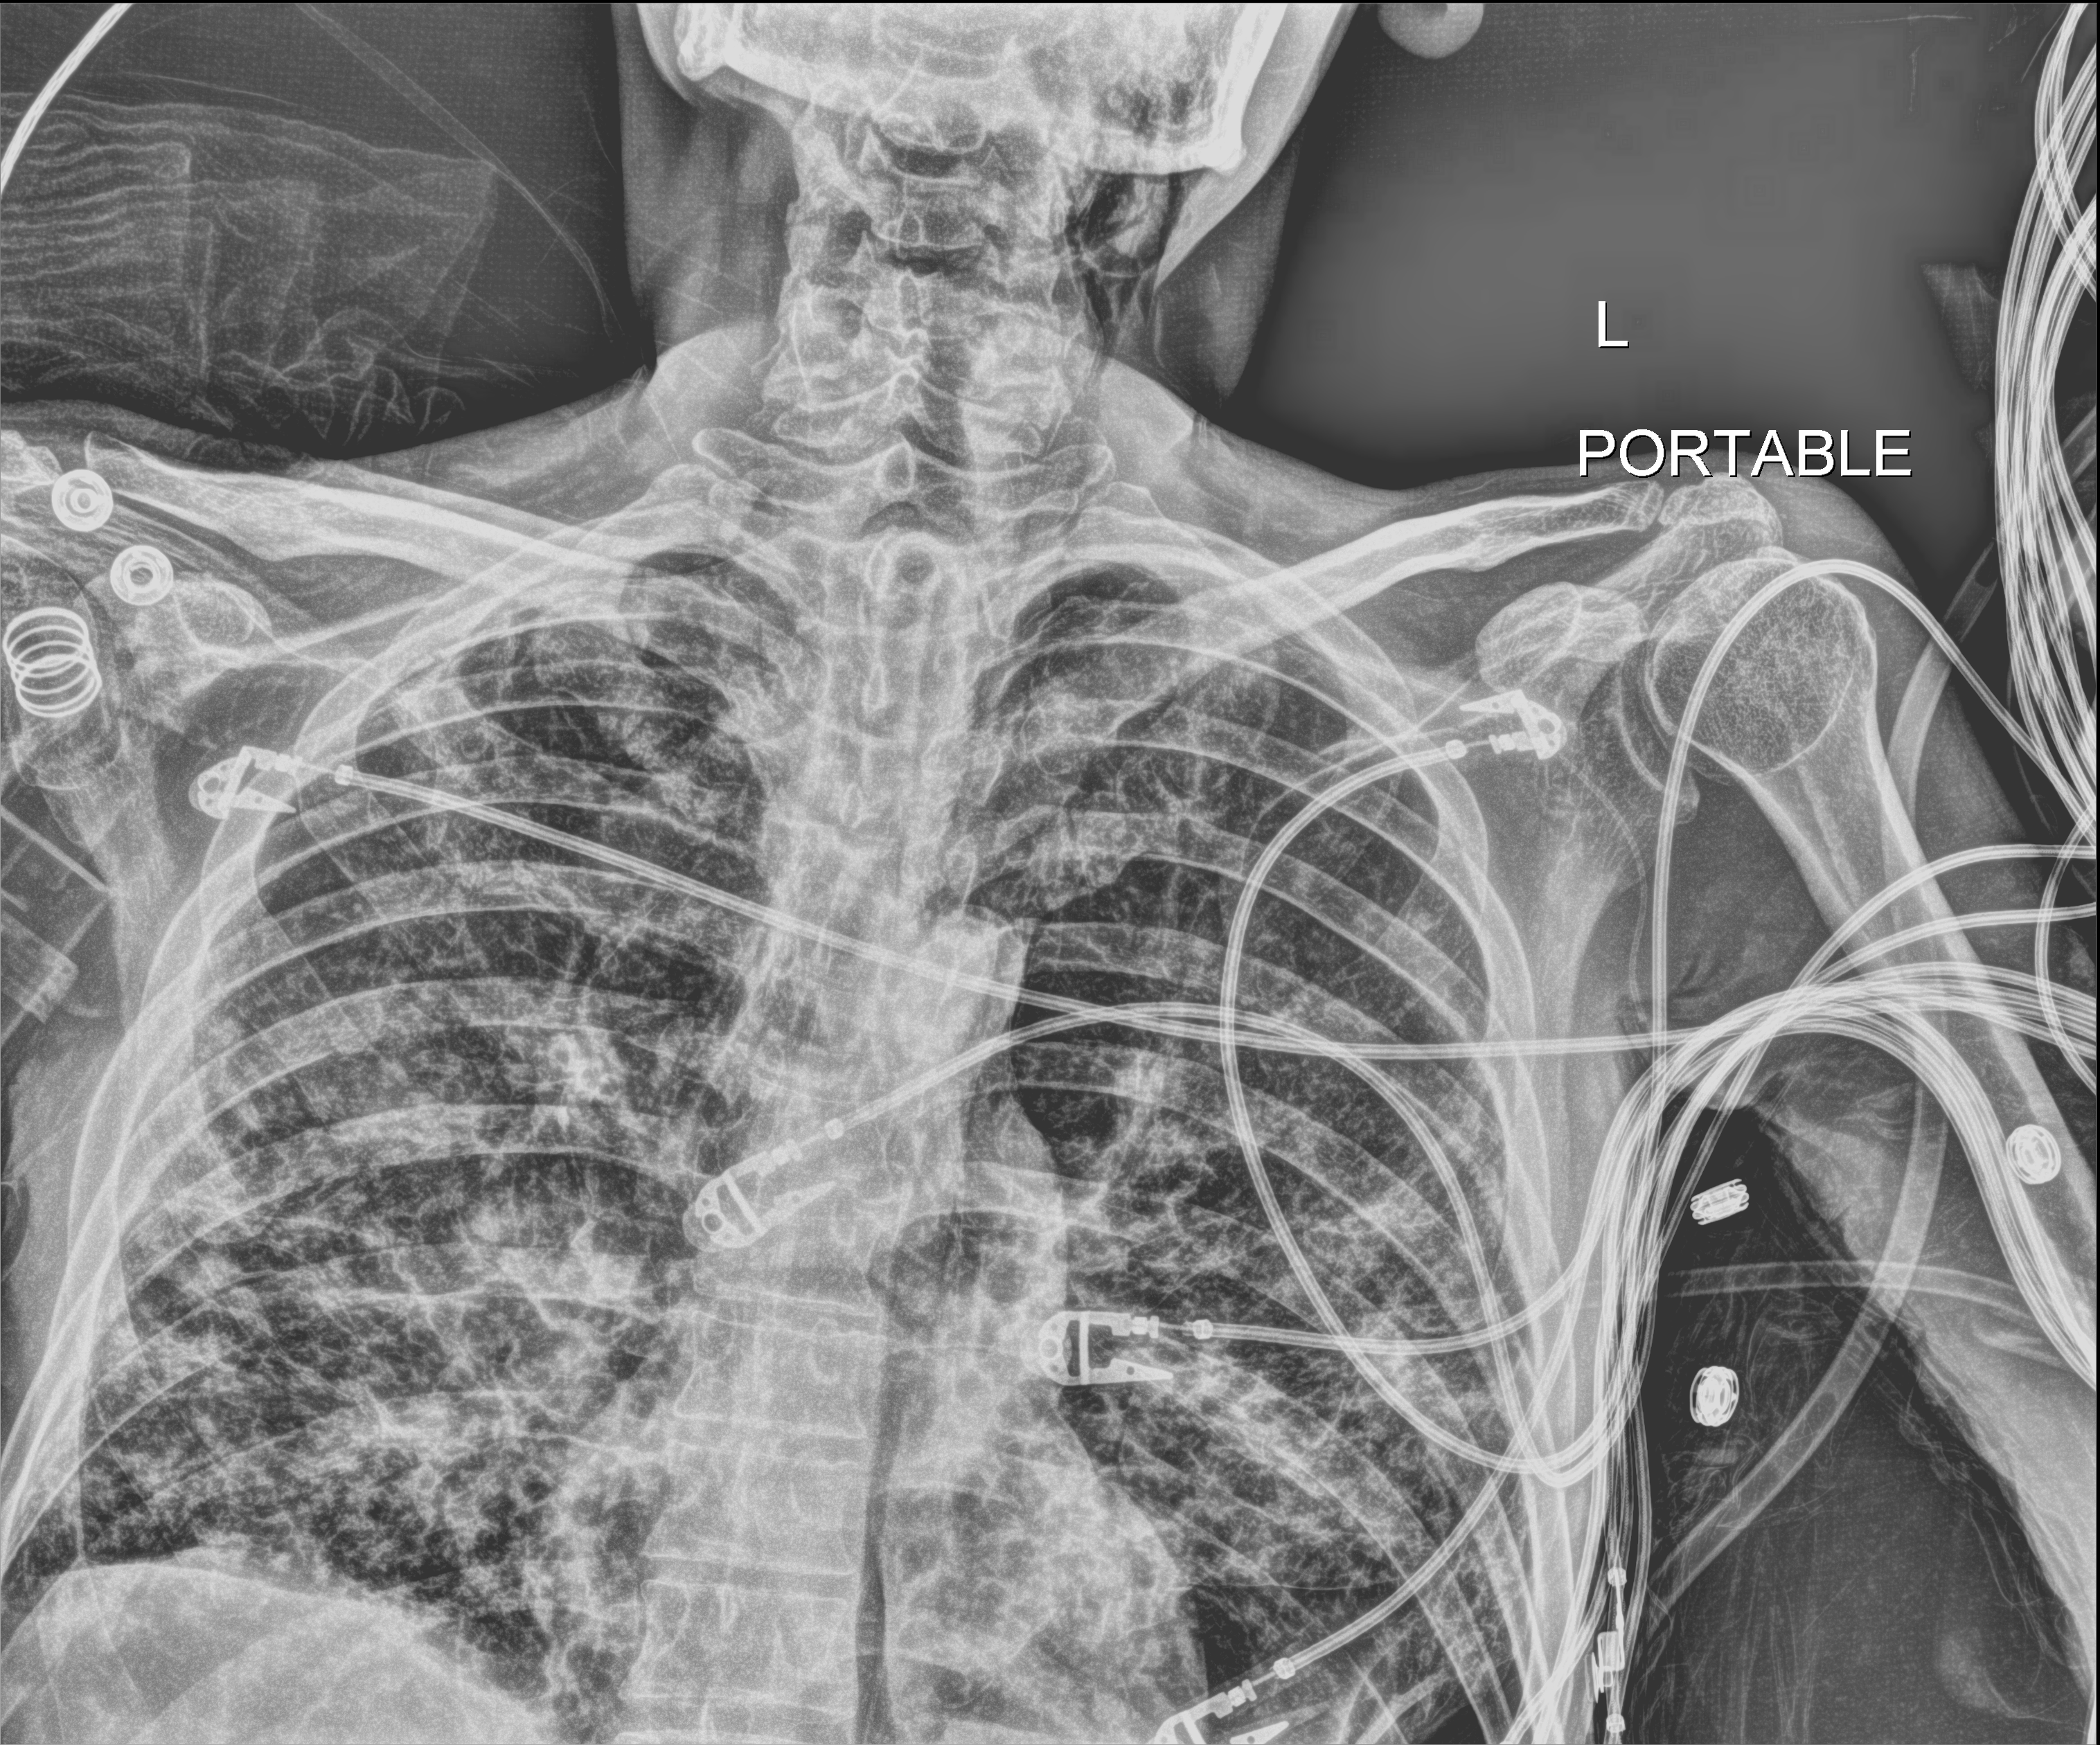
Chest radiograph; anteroposterior (AP) projection. Patient hospitalised with COVID-19; male, aged 18–59 years.
Hospital-stay facts (about this admission, not read from this image; timing relative to this image not recorded): length of hospital stay: 96 days; mechanically ventilated during this hospital stay: yes; admitted to intensive care during this hospital stay: yes.